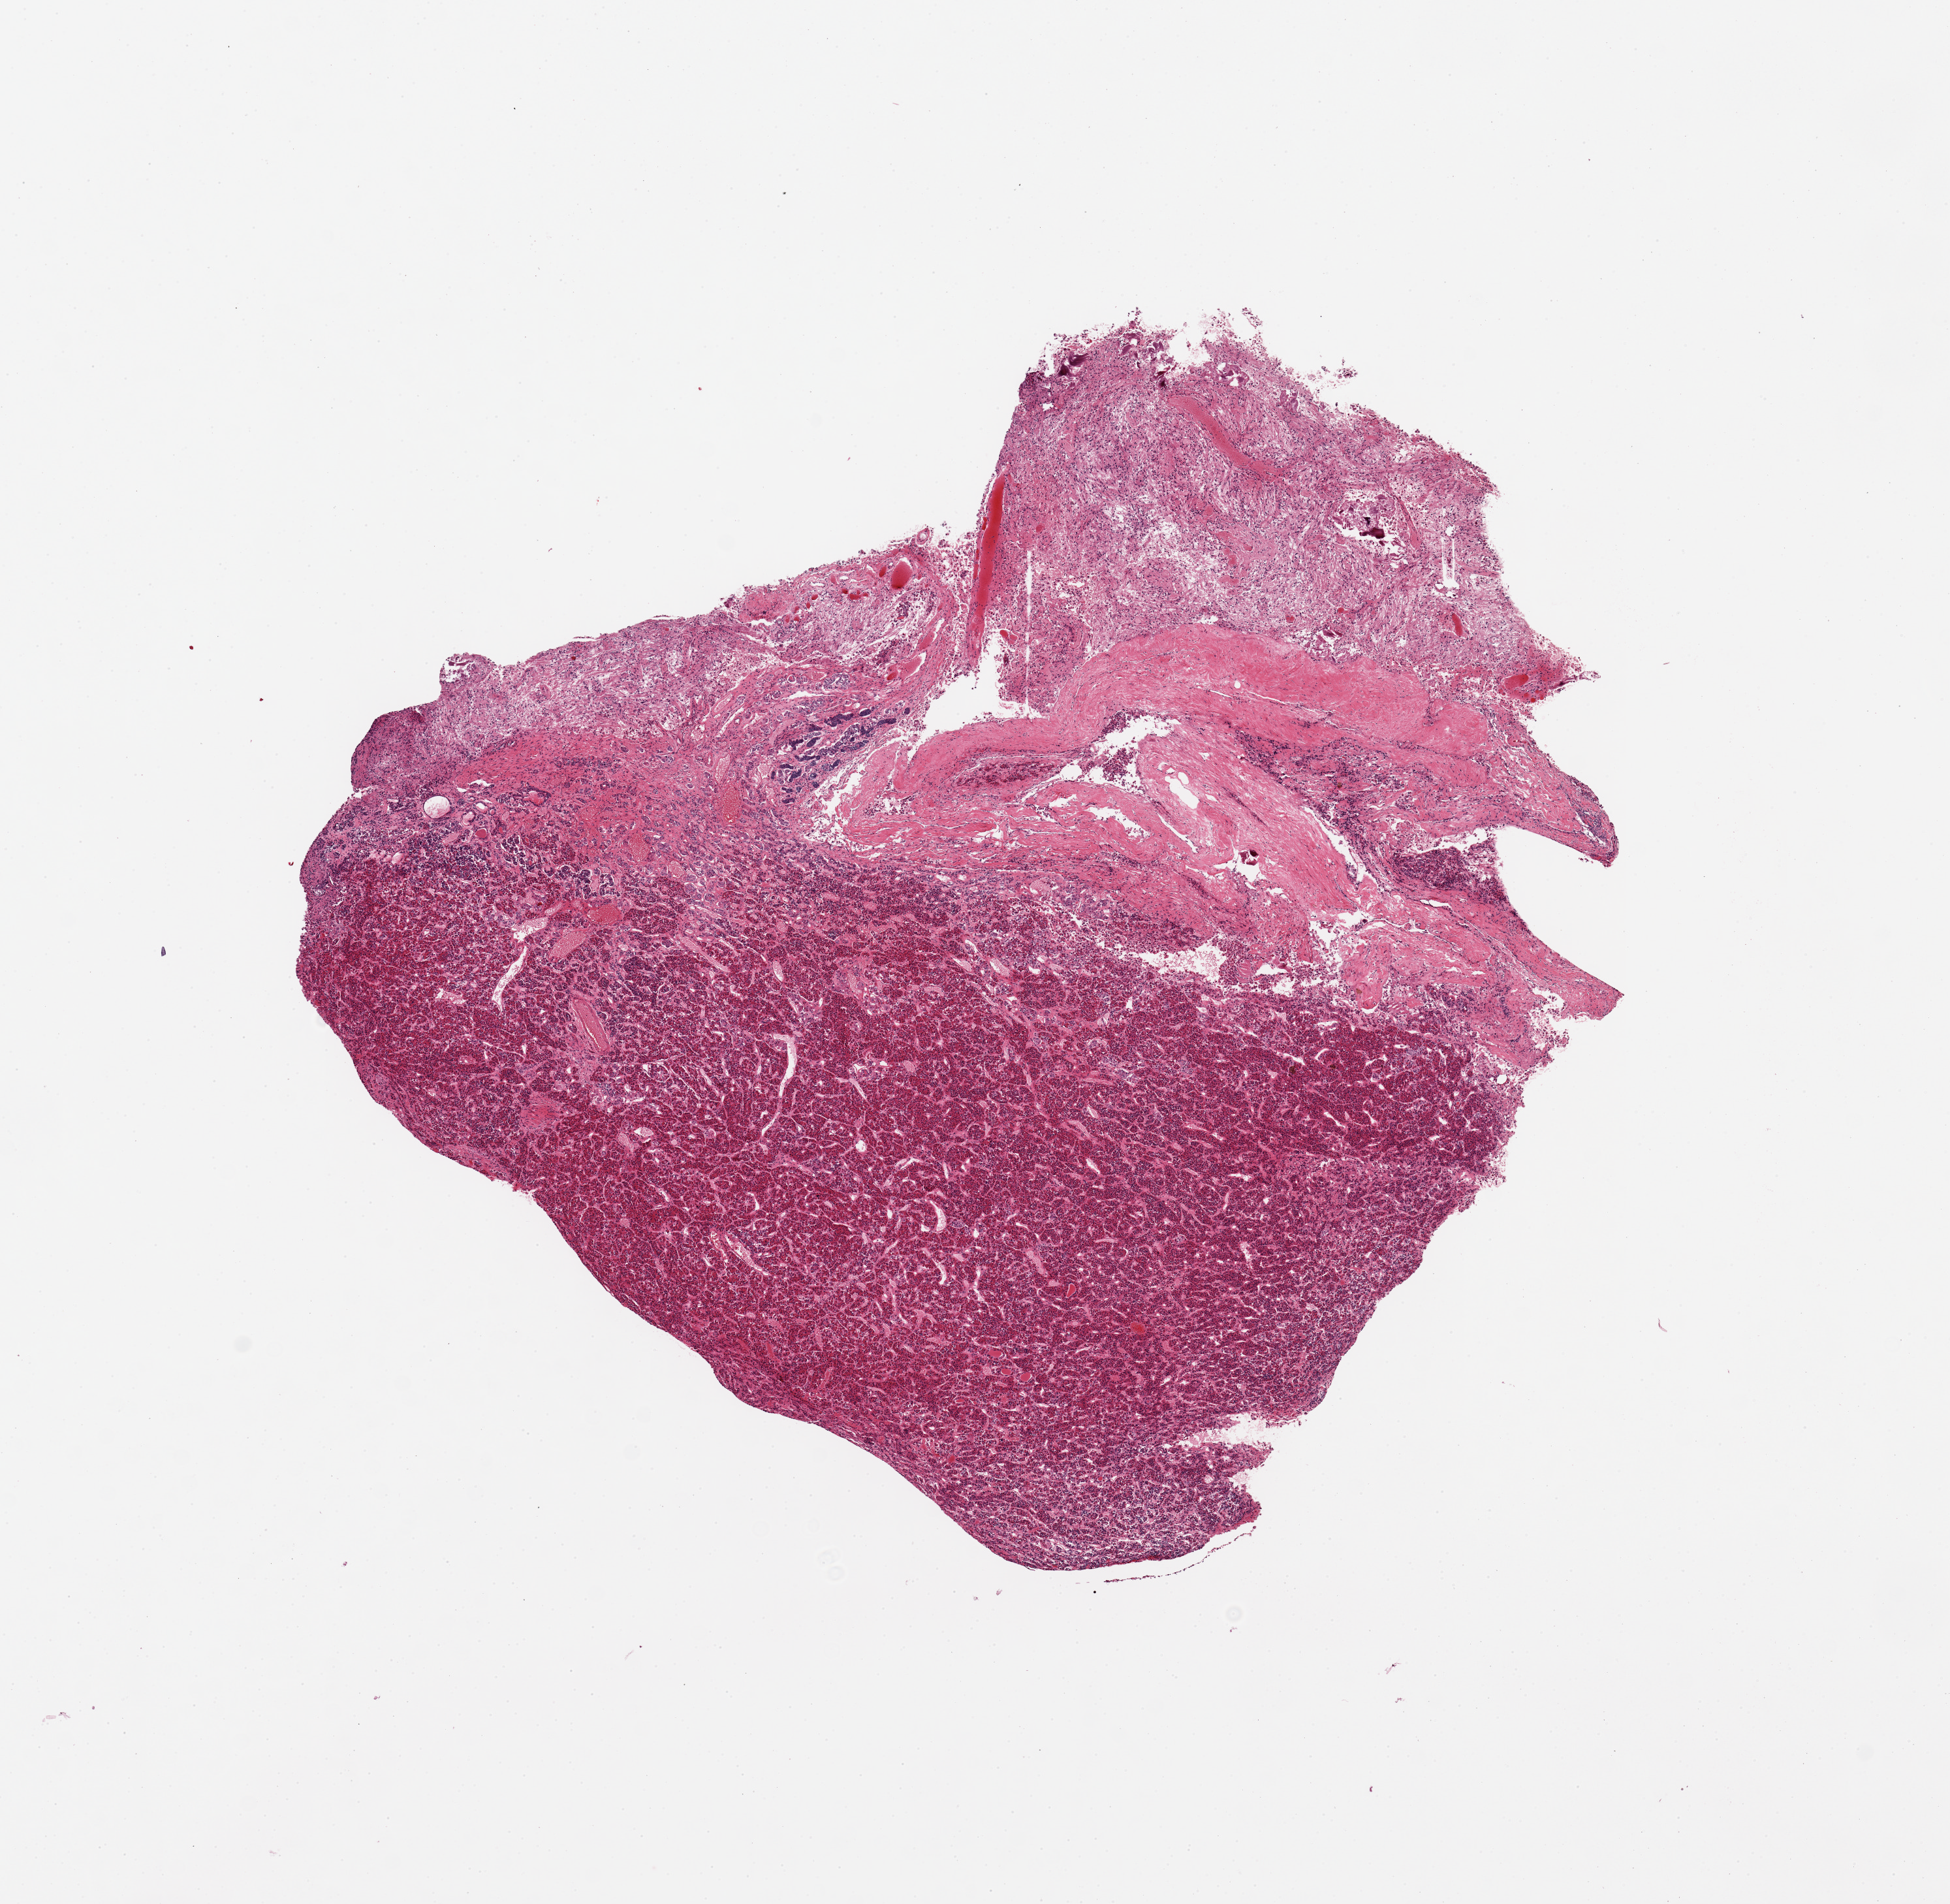
Whole-slide image, H&E stain, whole scanned area (about 11.8 x 11.5 mm, from a 20x scan) shown as a low-resolution overview, PAXgene-fixed, paraffin-embedded tissue, section of pituitary (target tissue), tissue donor sample. Female donor.
Pathologist's review note for this sample: 1 piece, ~50% neurohypophysis; rest adenohypophysis.